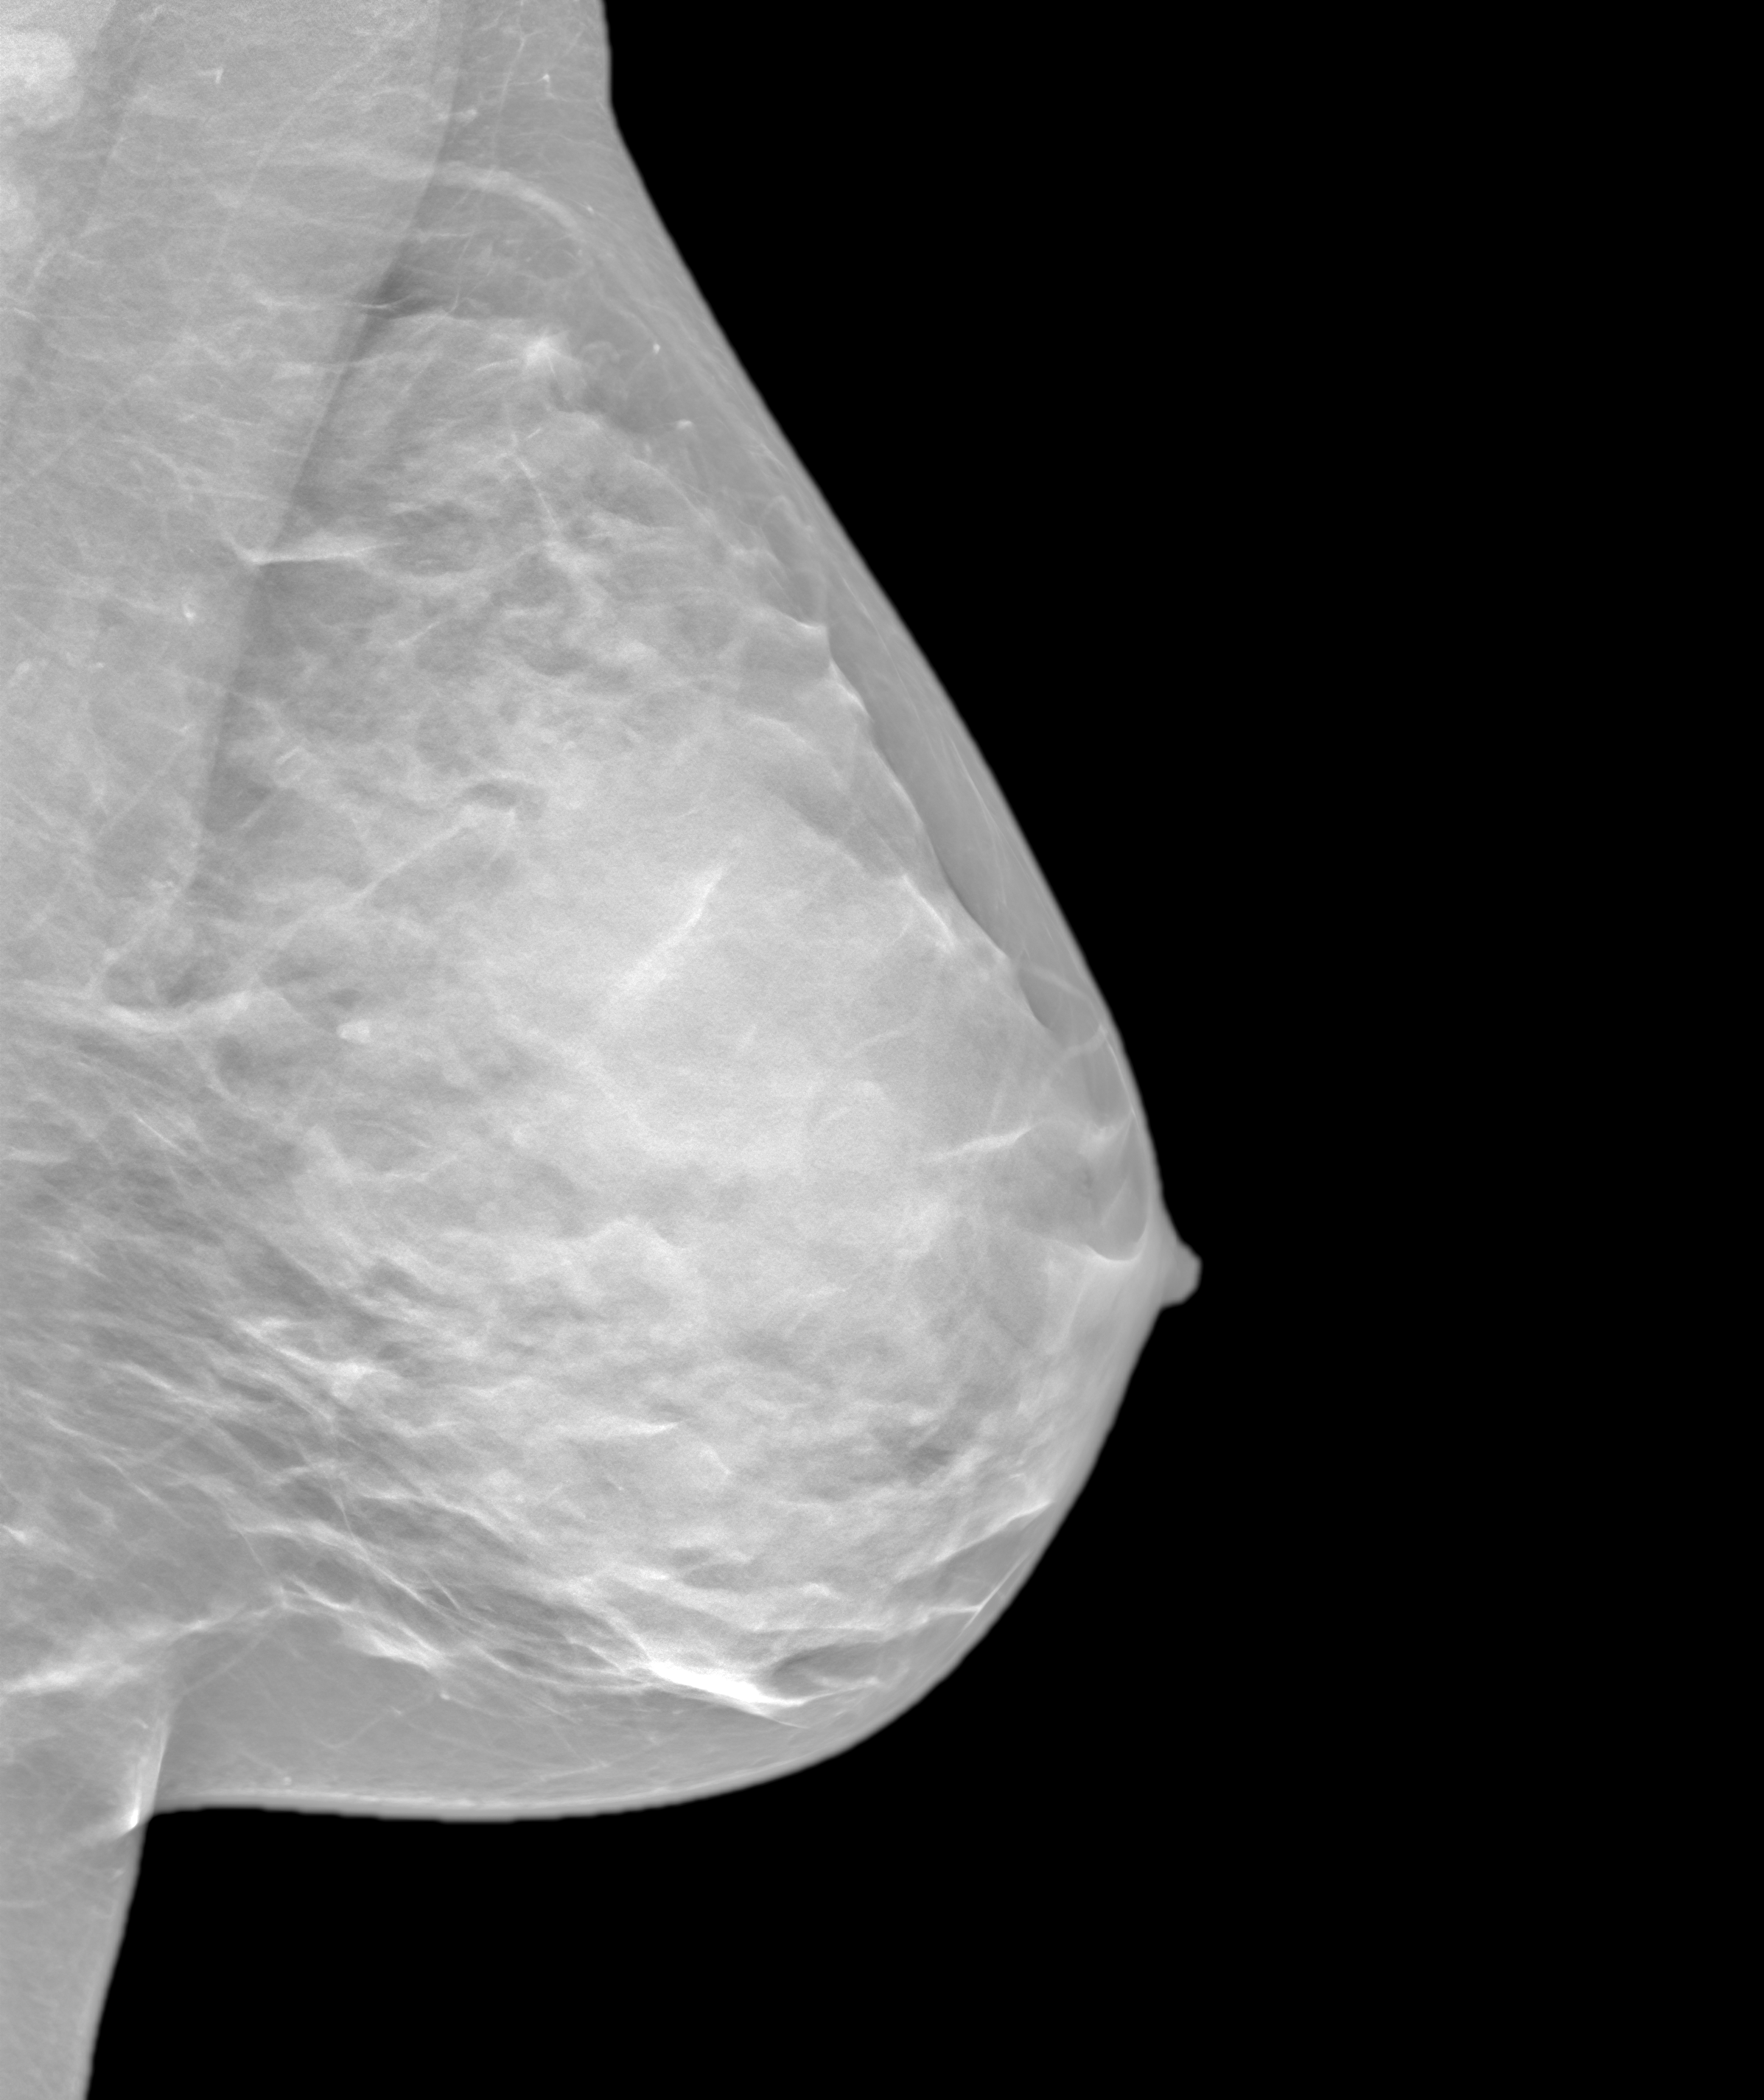
Screening examination, system: SenoIris_1SP1.1(421). Patient aged 44 years (female).
Image type: synthesized 2-D view from tomosynthesis. Breast: left. Projection: mediolateral oblique (MLO) view.